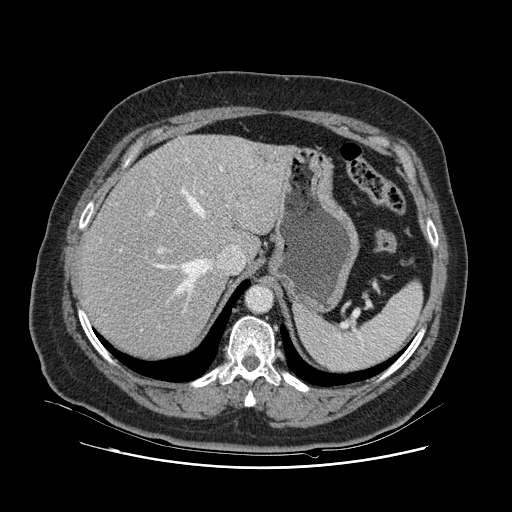
Contrast-enhanced abdominal CT, one axial slice. Position 88 of 132 along the scan axis. 120 kVp. Intravenous contrast given. Soft-tissue window (W 400 / L 40 HU). 2.5 mm slice thickness. 512 × 512 image matrix, field of view 391 × 391 mm. Female patient, age 73 years. Case-level facts recorded for this patient, not image findings: diagnosis: colorectal cancer liver metastases, imaged before liver resection; multiple liver metastases: no.
Outlined on this slice (manually delineated by an expert):
- hepatic veins: bounding box (x1, y1, x2, y2) in pixels: (141, 167, 236, 331)
- liver: (82, 135, 290, 358)
- planned liver remnant (the part of the liver to remain after resection): (82, 161, 249, 359)
- portal vein (with intrahepatic branches): (119, 158, 189, 327)